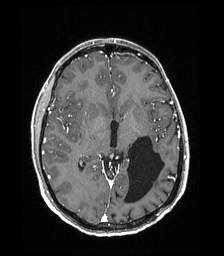
Brain MRI from a brain-tumour surgery series, one axial slice; position 99 of 192 along the scan axis; T1-weighted post-contrast; 1 mm slice thickness; 224 × 256 image matrix, field of view 224 × 256 mm. From the clinical record (not read from this slice): histopathology: Low grade glioma; IDH mutation: no.
Structures marked on this image (manually delineated by an expert):
- previous resection cavity: bounding box (x1, y1, x2, y2) in pixels: (125, 136, 164, 203)